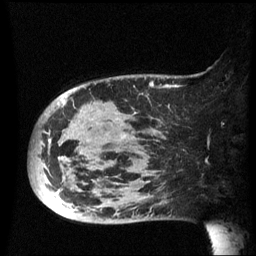
Breast MRI (dynamic contrast-enhanced), one sagittal slice; position 17 of 60 along the scan axis; dynamic contrast-enhanced series, image 2 of 3 at this slice position (ordered by acquisition); 1.5 T; TE 4.2 ms, TR 8.4 ms; 2.5 mm slice thickness; 256 × 256 image matrix, field of view 220 × 220 mm. Female patient, age 49 years.
Structures marked on this image (semi-automatically segmented with operator editing):
- analysis volume of interest (the breast-tissue region the enhancement analysis was run in; not a lesion): bounding box [x1, y1, x2, y2] px = [29, 74, 183, 225]
- tumour enhancement mask (voxels above the 70 % enhancement threshold inside the analysis volume of interest): [49, 84, 152, 153]